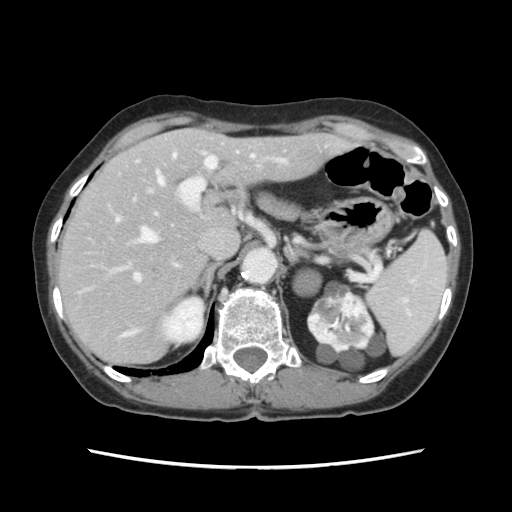
Contrast-enhanced abdominal CT, one axial slice. Slice 83 of 120 in the series (ordered by position). 120 kVp. Intravenous contrast given. Soft-tissue window (W 400 / L 40 HU). 2.5 mm slice thickness. 512 × 512 image matrix, field of view 330 × 330 mm. Female patient, age 70 years. From the clinical record (not read from this slice): diagnosis: colorectal cancer liver metastases, imaged before liver resection; multiple liver metastases: no; largest metastasis: 2.5 cm; disease in both lobes: no.
Annotated regions visible in this slice (outlined manually by an expert reader):
- hepatic veins: bounding box [x1, y1, x2, y2] px = [139, 154, 176, 243]
- liver: [59, 129, 343, 363]
- planned liver remnant (the part of the liver to remain after resection): [102, 128, 343, 289]
- portal vein (with intrahepatic branches): [112, 152, 285, 281]